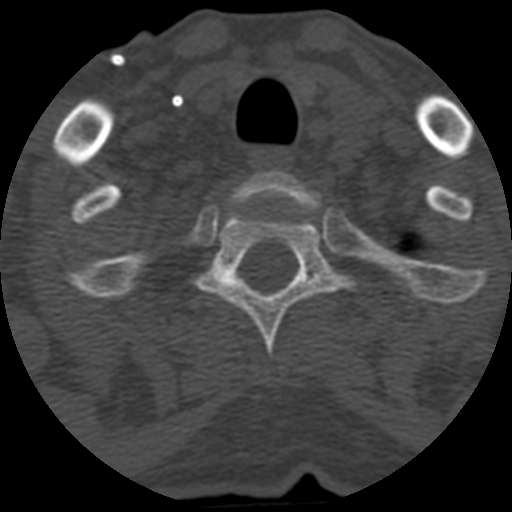
CT including the spine, one axial slice; slice 506 of 708 in the series (ordered by position); 120 kVp; one of 3 acquisitions stored at this slice position; bone window (W 1800 / L 400 HU); 1.25 mm slice thickness; 512 × 512 image matrix, field of view 160 × 160 mm. Patient age 55 years. From the clinical record (not read from this slice): primary cancer: colon.
Outlined on this slice (semi-automatic segmentation, software-assisted and operator-edited):
- T1 vertebra: bounding box <237,171,314,207> (left, top, right, bottom; pixels)
- T2 vertebra: <197,209,353,359>